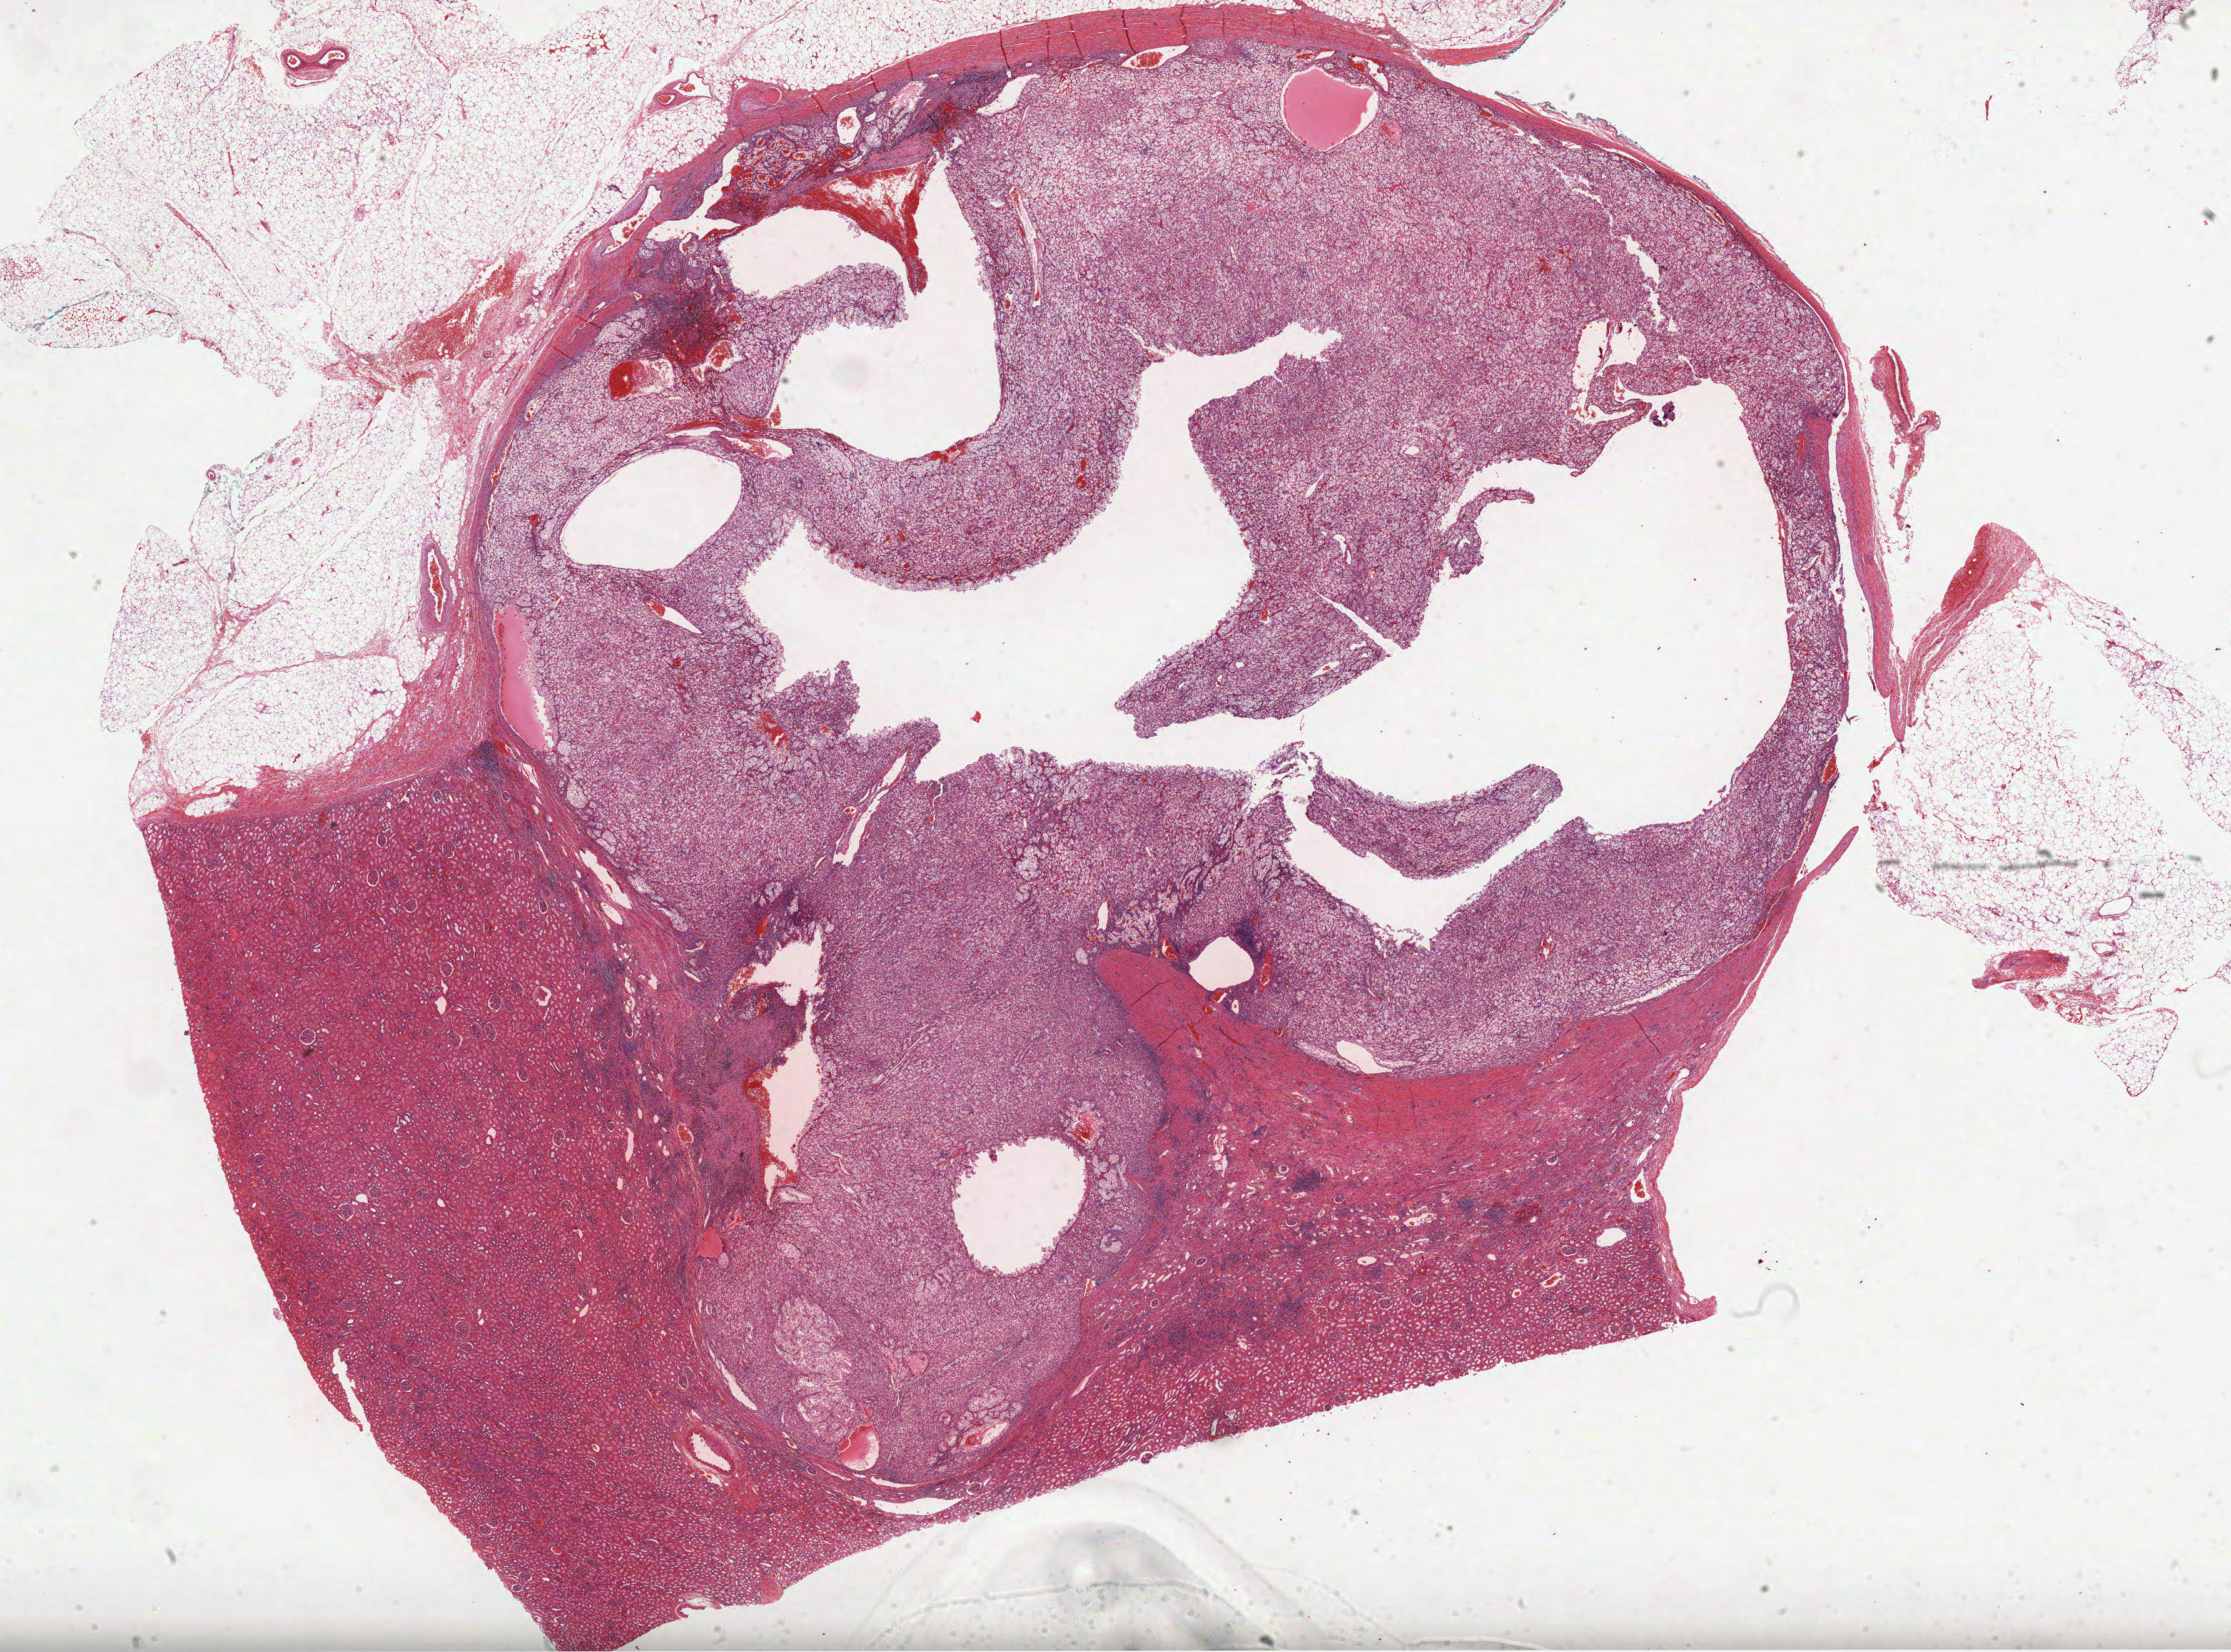
H&E-stained whole-slide image — whole scanned area (about 28.8 x 21.3 mm, acquisition: 40x scan) shown as a low-resolution overview. Formalin-fixed paraffin-embedded (FFPE) diagnostic section. Primary tumour sample from the kidney. Male patient; age at initial diagnosis 50 years. Histologic grade: G2 (moderately differentiated).
- AJCC pathologic stage: I (6th edition)
- laterality: right
- diagnosis: Clear cell adenocarcinoma, NOS